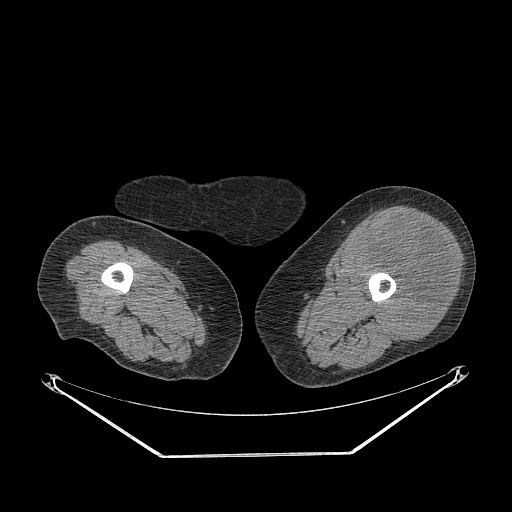
CT of an extremity soft-tissue mass (from a PET/CT study), one axial slice. Position 223 of 267 along the scan axis. Soft-tissue window (W 400 / L 40 HU). 3.75 mm slice thickness. 512 × 512 image matrix, field of view 500 × 500 mm. Female patient. Case-level facts recorded for this patient, not image findings: histological type: undifferentiated – high grade; grade: high; site of the primary tumour: left thigh.
Outlined on this slice (expert contour drawn on MRI and transferred to this co-registered scan by the dataset authors):
- gross tumour volume including surrounding oedema: bounding box [x1, y1, x2, y2] px = [354, 217, 453, 341]
- gross tumour volume (mass): [354, 217, 453, 341]